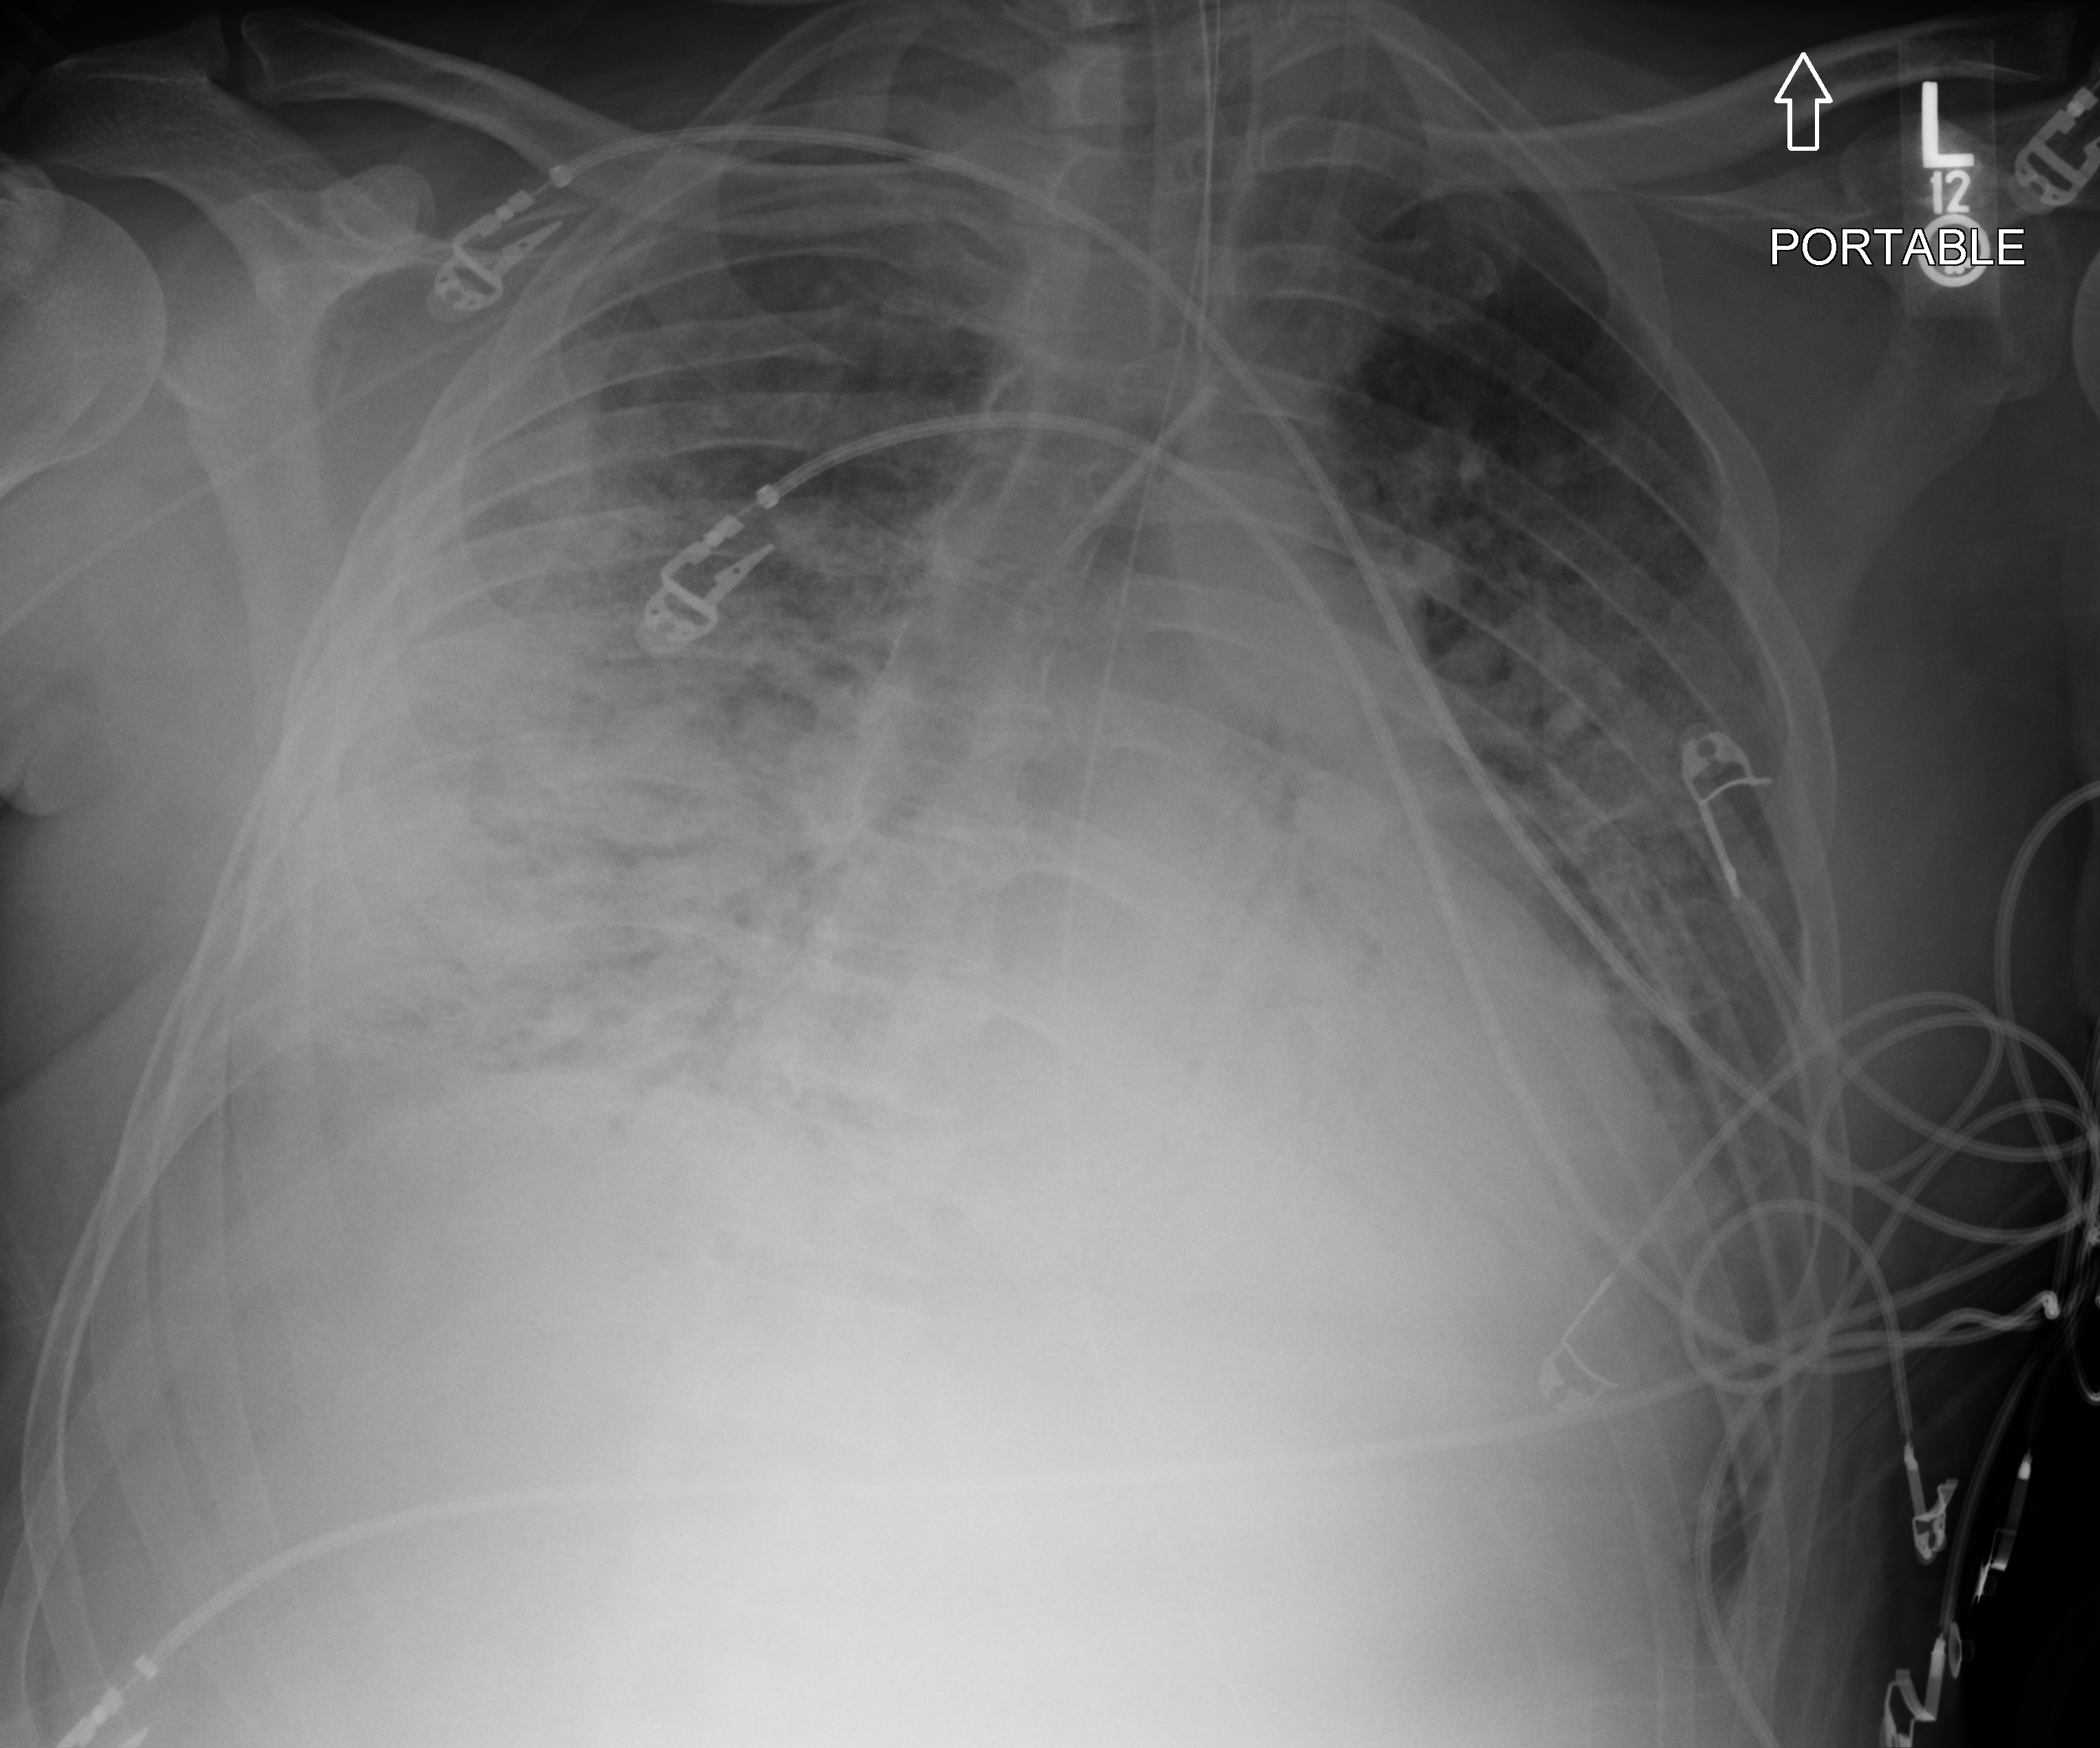
Bedside chest radiograph (computed radiography); anteroposterior (AP) projection. Patient hospitalised with COVID-19; male, aged 18–59 years.
Admission-level facts for this patient (not findings on this image; timing relative to this image not recorded): COPD (admission record): no.